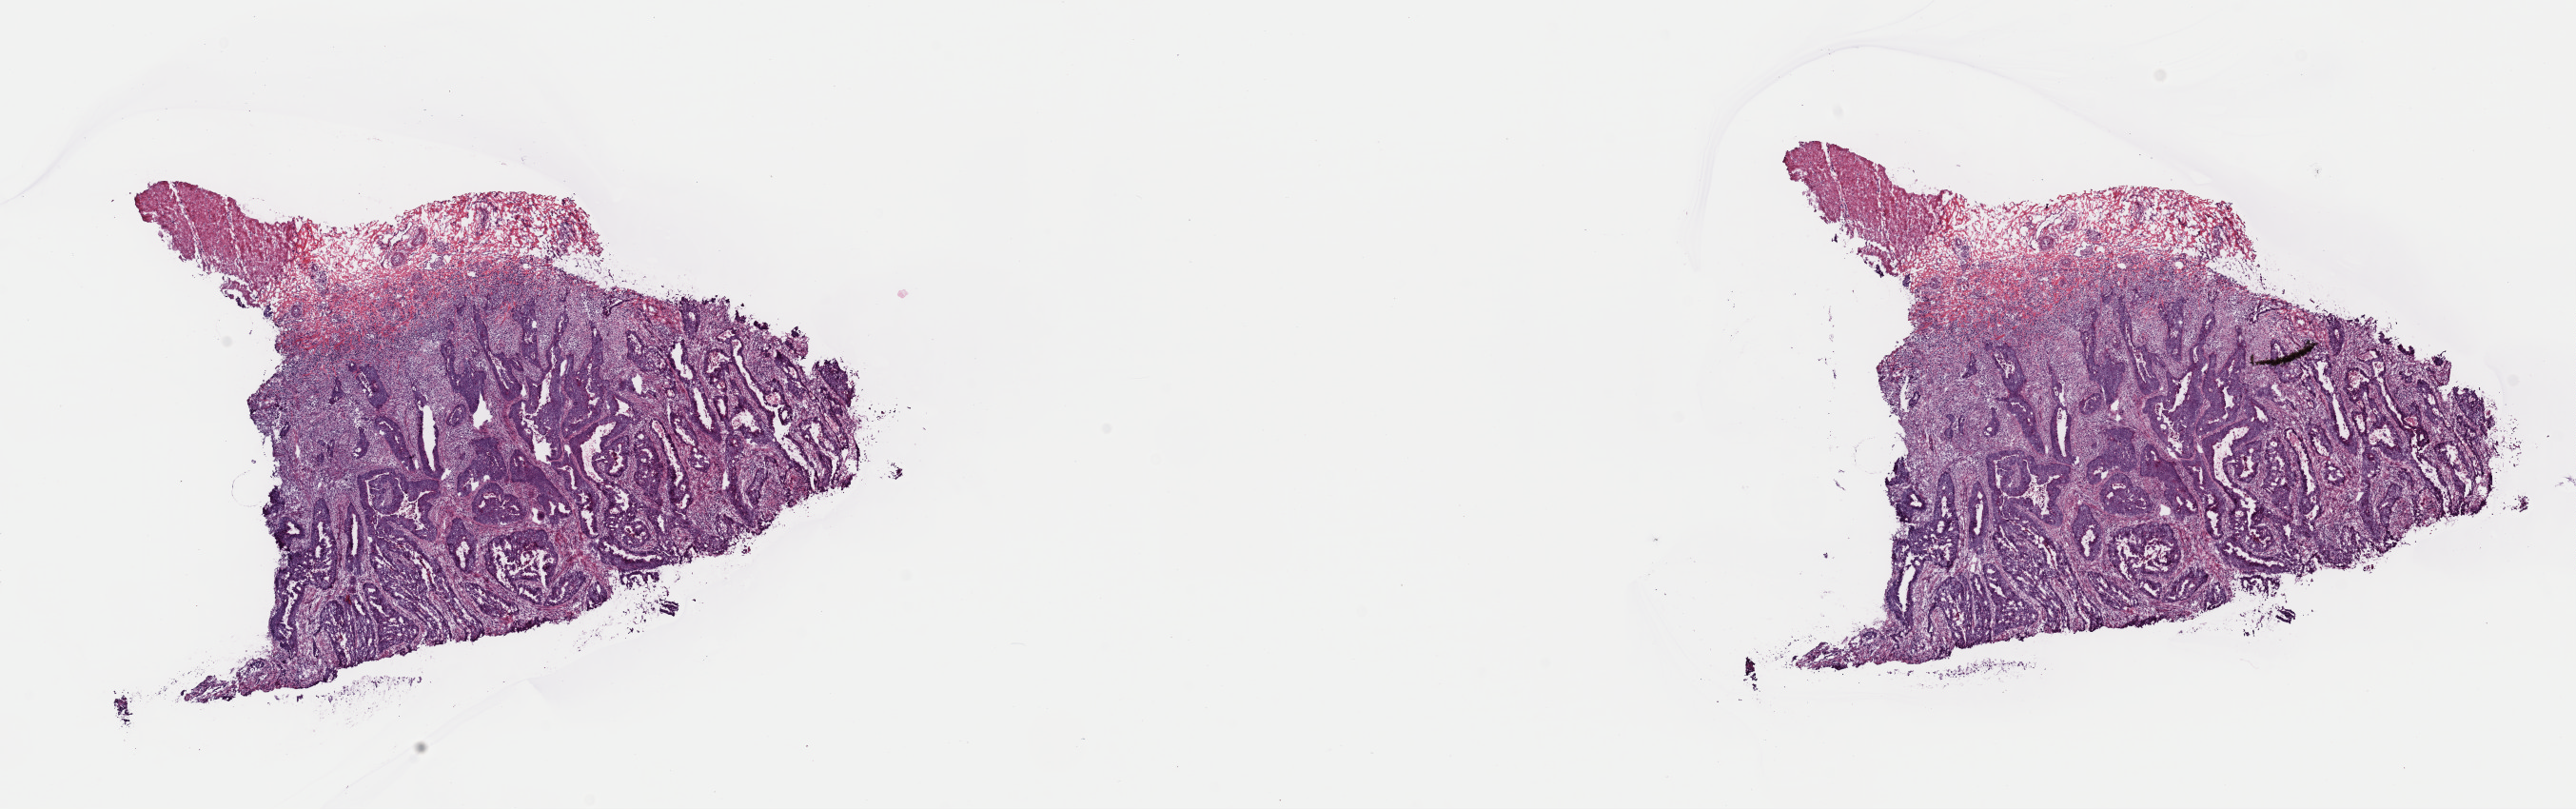
Whole-slide histology image, H&E-stained, low-resolution overview of the scanned area, about 21.4 x 6.7 mm; frozen section from the top of the tissue portion; rectum, primary tumour sample. Female, age 48 years at initial diagnosis. Composition of this section per pathologist review: tumour cells 85%, tumour nuclei 60%, normal cells 12%, stromal cells 0%, necrosis 3%. Infiltration values recorded for this section: lymphocyte infiltration 5%, monocyte infiltration 0%, neutrophil infiltration 1%.
• lymph nodes positive (case pathology): 10 of 23 examined
• pathologic diagnosis: Adenocarcinoma, NOS (rectosigmoid junction)
• AJCC pathologic stage: IIIC (6th edition)